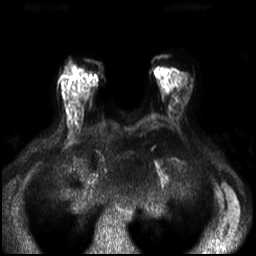
Breast MRI, one axial slice; position 14 of 30 along the scan axis; diffusion-weighted series; image 2 of 4 stored at this slice position (different b-values; order by instance number); 3 T; 4 mm slice thickness; 256 × 256 image matrix, field of view 320 × 320 mm. Female patient.
Outlined on this slice (expert manual segmentation):
- tumour on diffusion-weighted imaging: box from (x=70, y=96) to (x=82, y=113) px